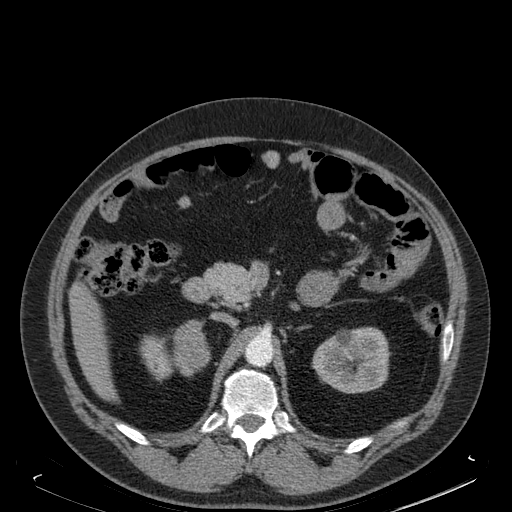
Contrast-enhanced abdominal CT, one axial slice. Slice 103 of 181 in the series (ordered by position). Soft-tissue window (W 400 / L 40 HU). 1.5 mm slice thickness. 512 × 512 image matrix, field of view 405 × 405 mm. Male patient. Case-level facts recorded for this patient, not image findings: diagnosis: adrenocortical carcinoma; tumour side: right adrenal; tumour size at pathology: 7.5 cm; Ki-67 index: 25 %; stage (as recorded): 4.
Structures marked on this image (semi-automatically segmented with operator editing):
- mass: box from (x=175, y=320) to (x=209, y=368) px